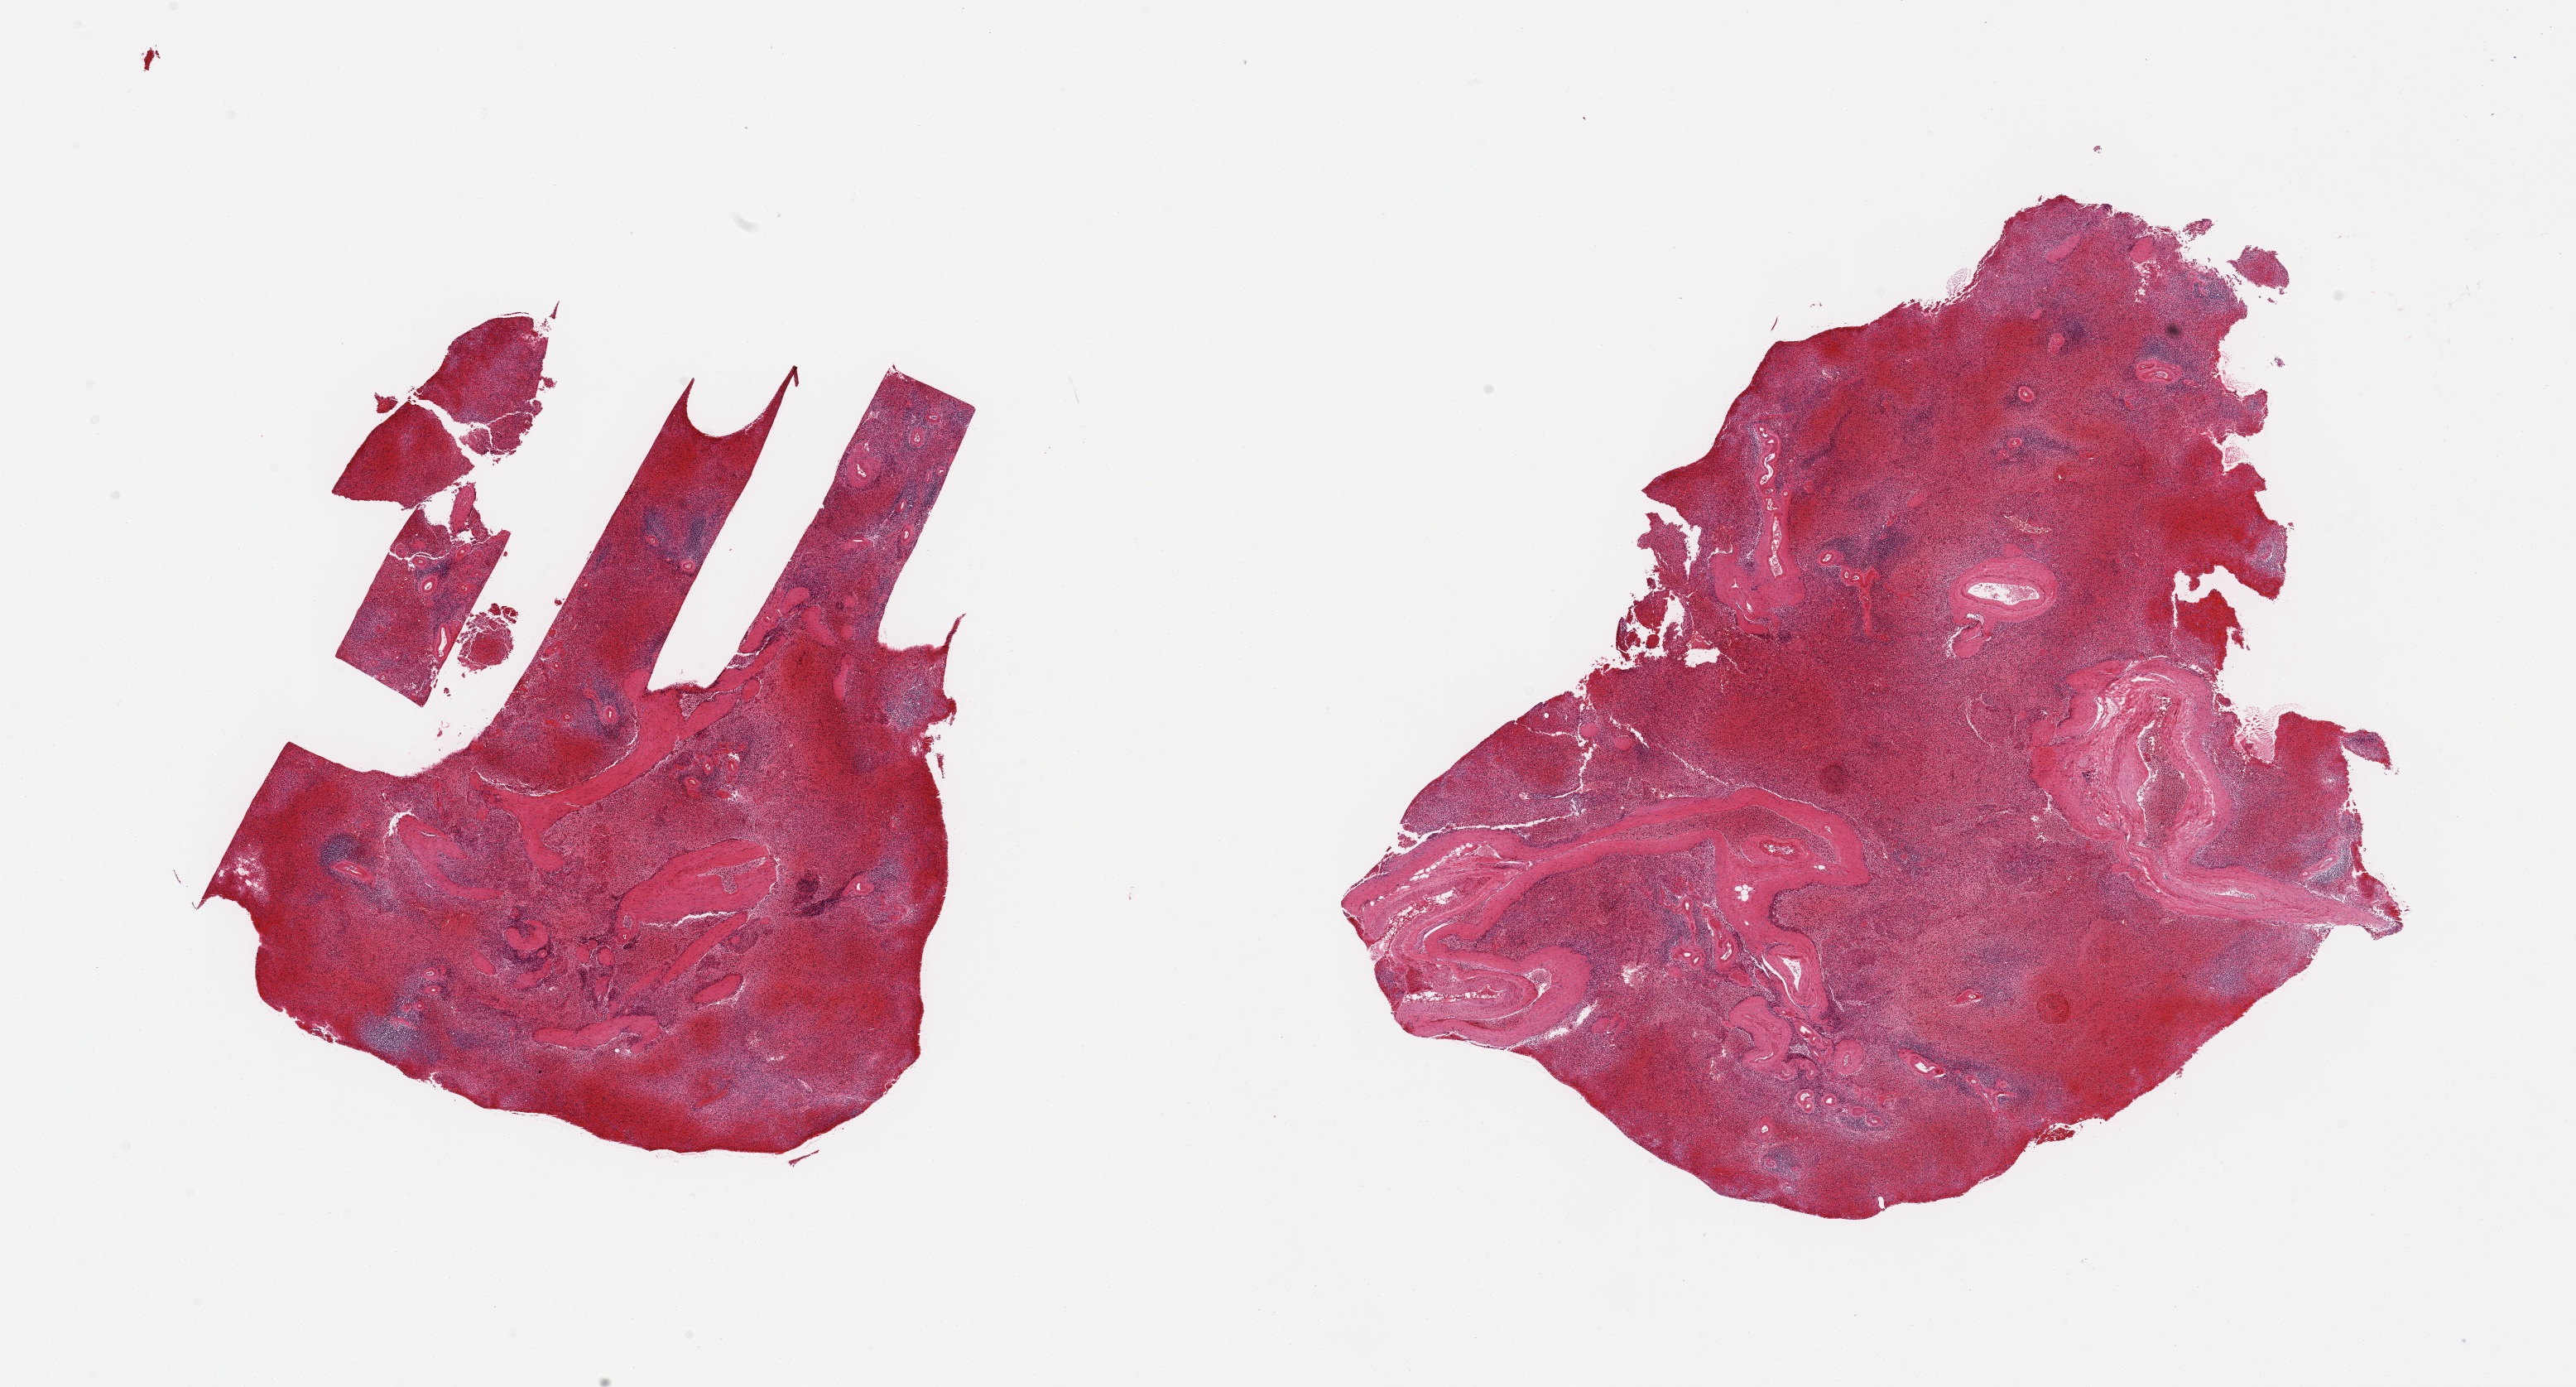
Whole-slide image, haematoxylin and eosin stain — low-resolution overview of the scanned area, about 24.6 x 13.2 mm. PAXgene-fixed paraffin-embedded (PFPE) section. Section of spleen (target tissue). Donor tissue sample.
Review note (as recorded): 2 pieces; moderately congested; numerous large blood vessels.